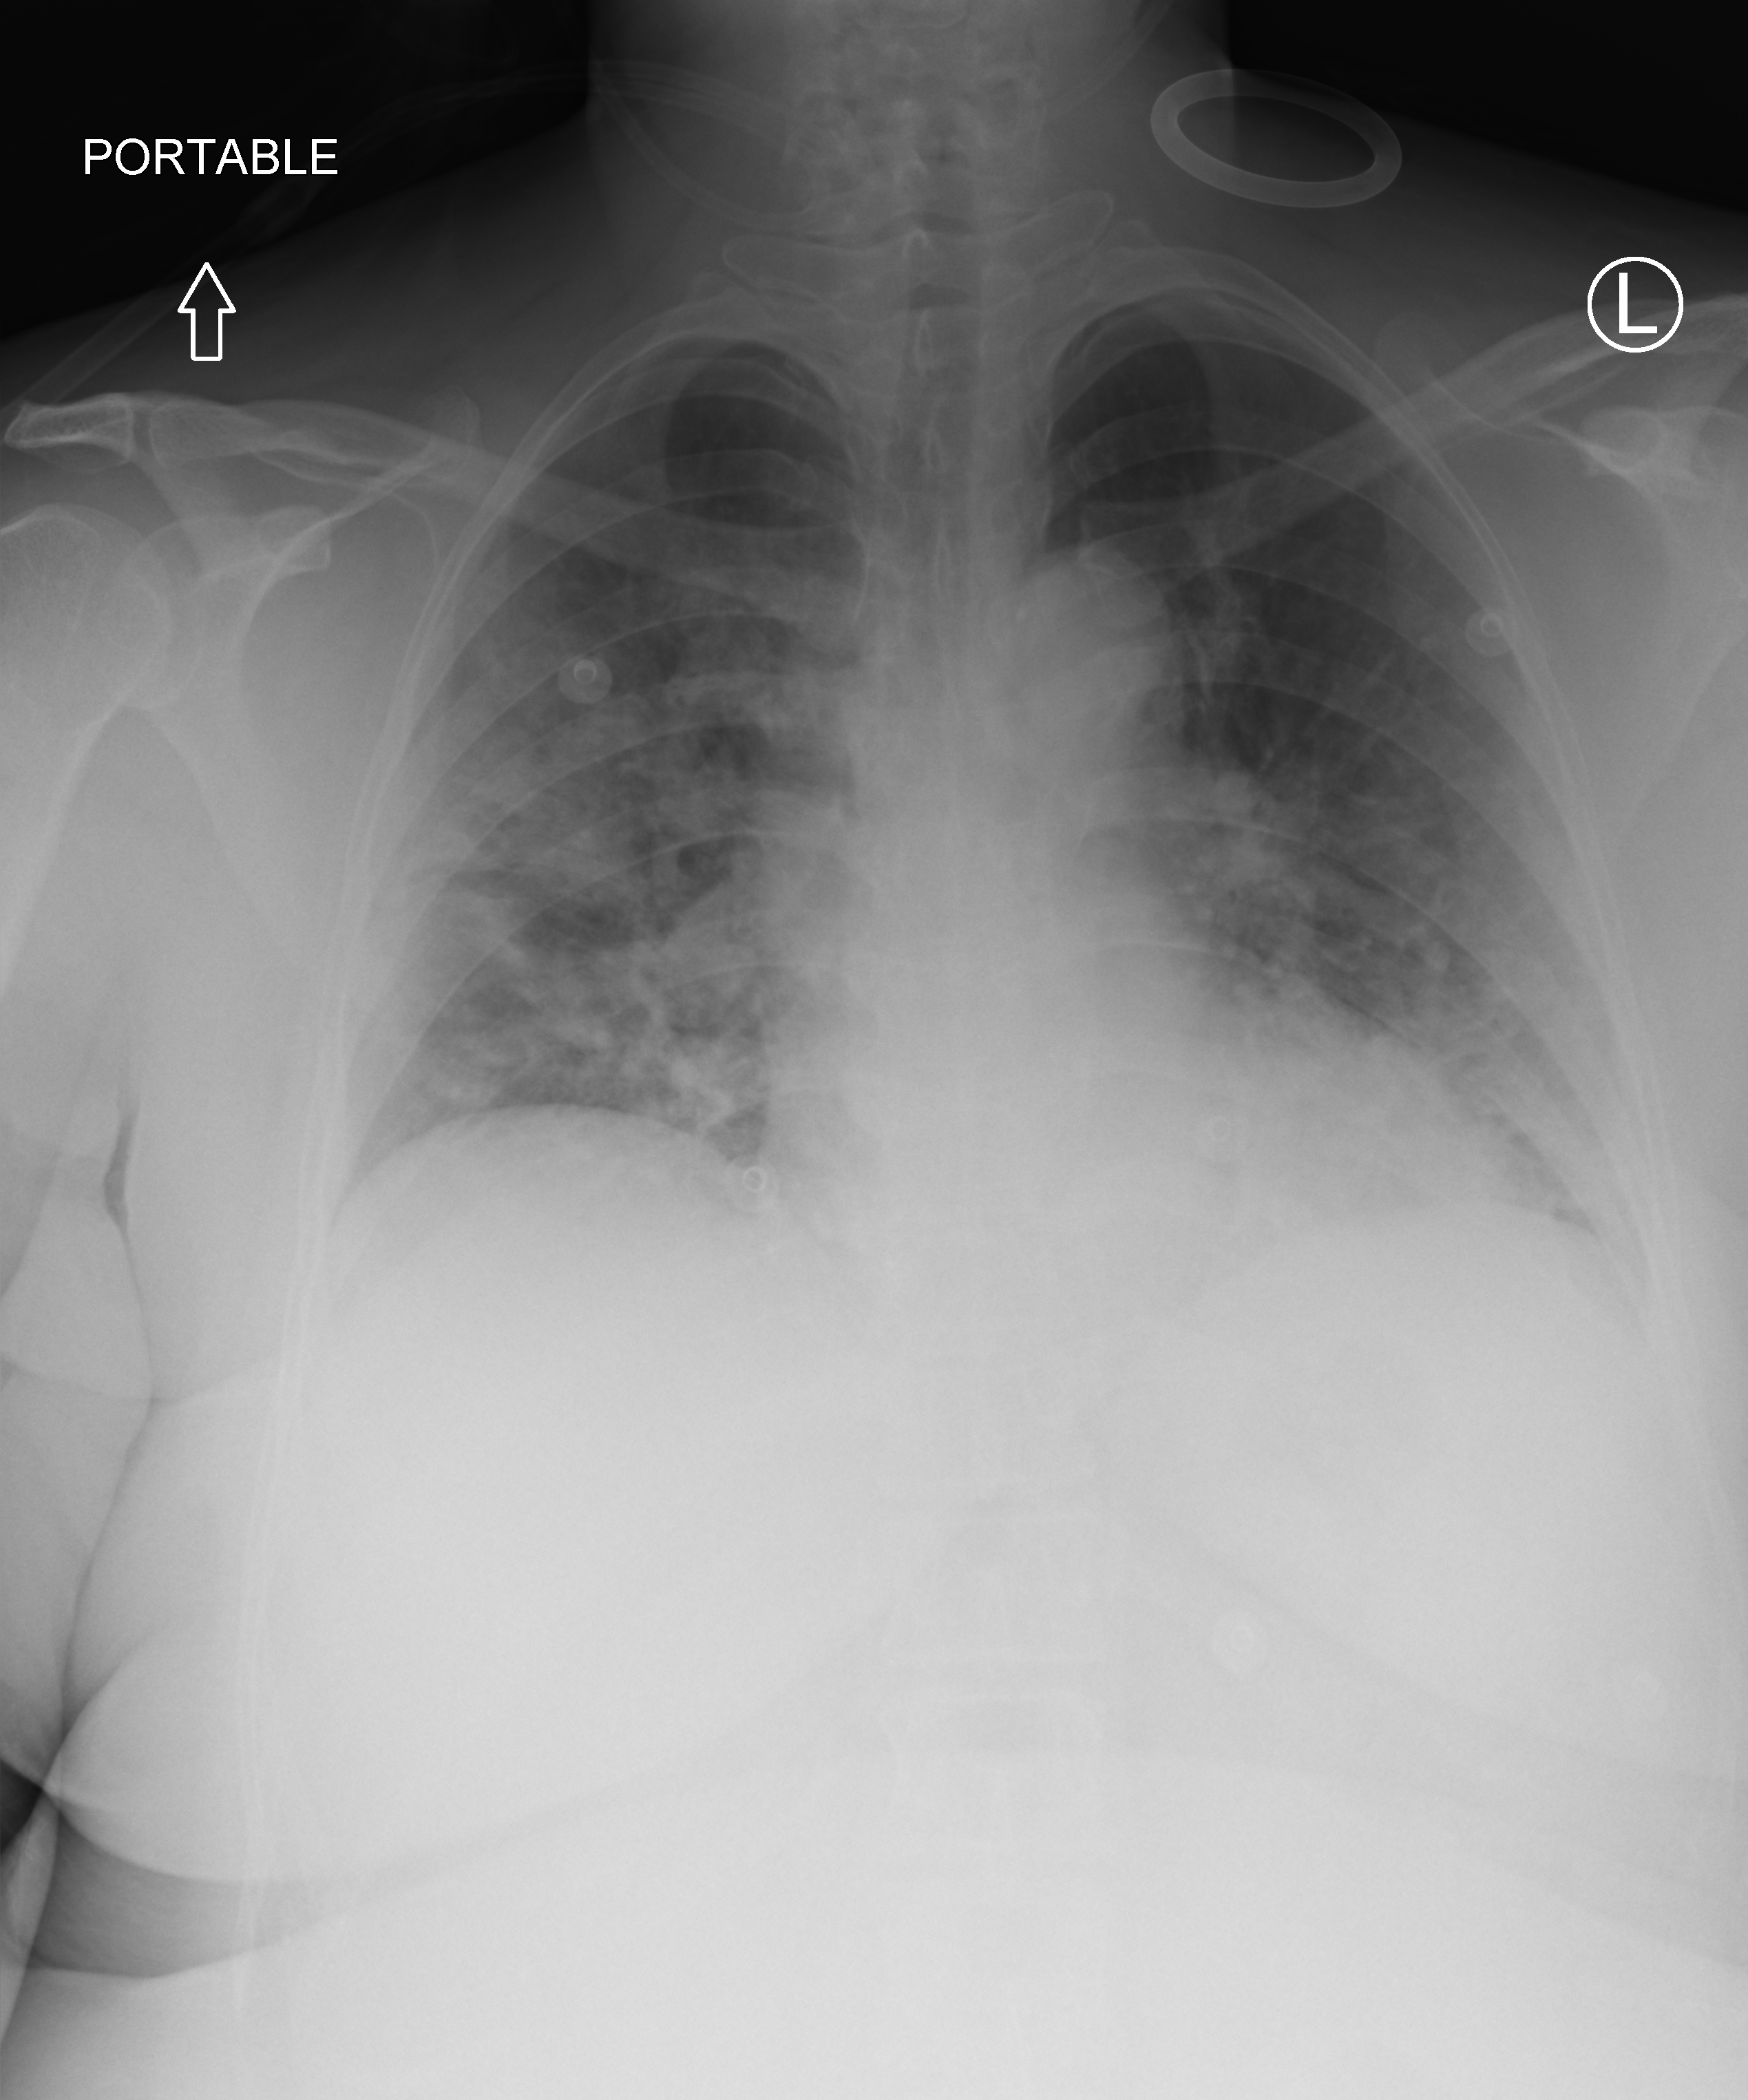
Bedside chest radiograph (computed radiography); anteroposterior (AP) projection. Female patient hospitalised with COVID-19, age 18–59 years.
Hospital-stay facts (about this admission, not read from this image; timing relative to this image not recorded):
- chronic kidney disease (admission record): no
- diabetes (admission record): no
- smoking status (admission record): never